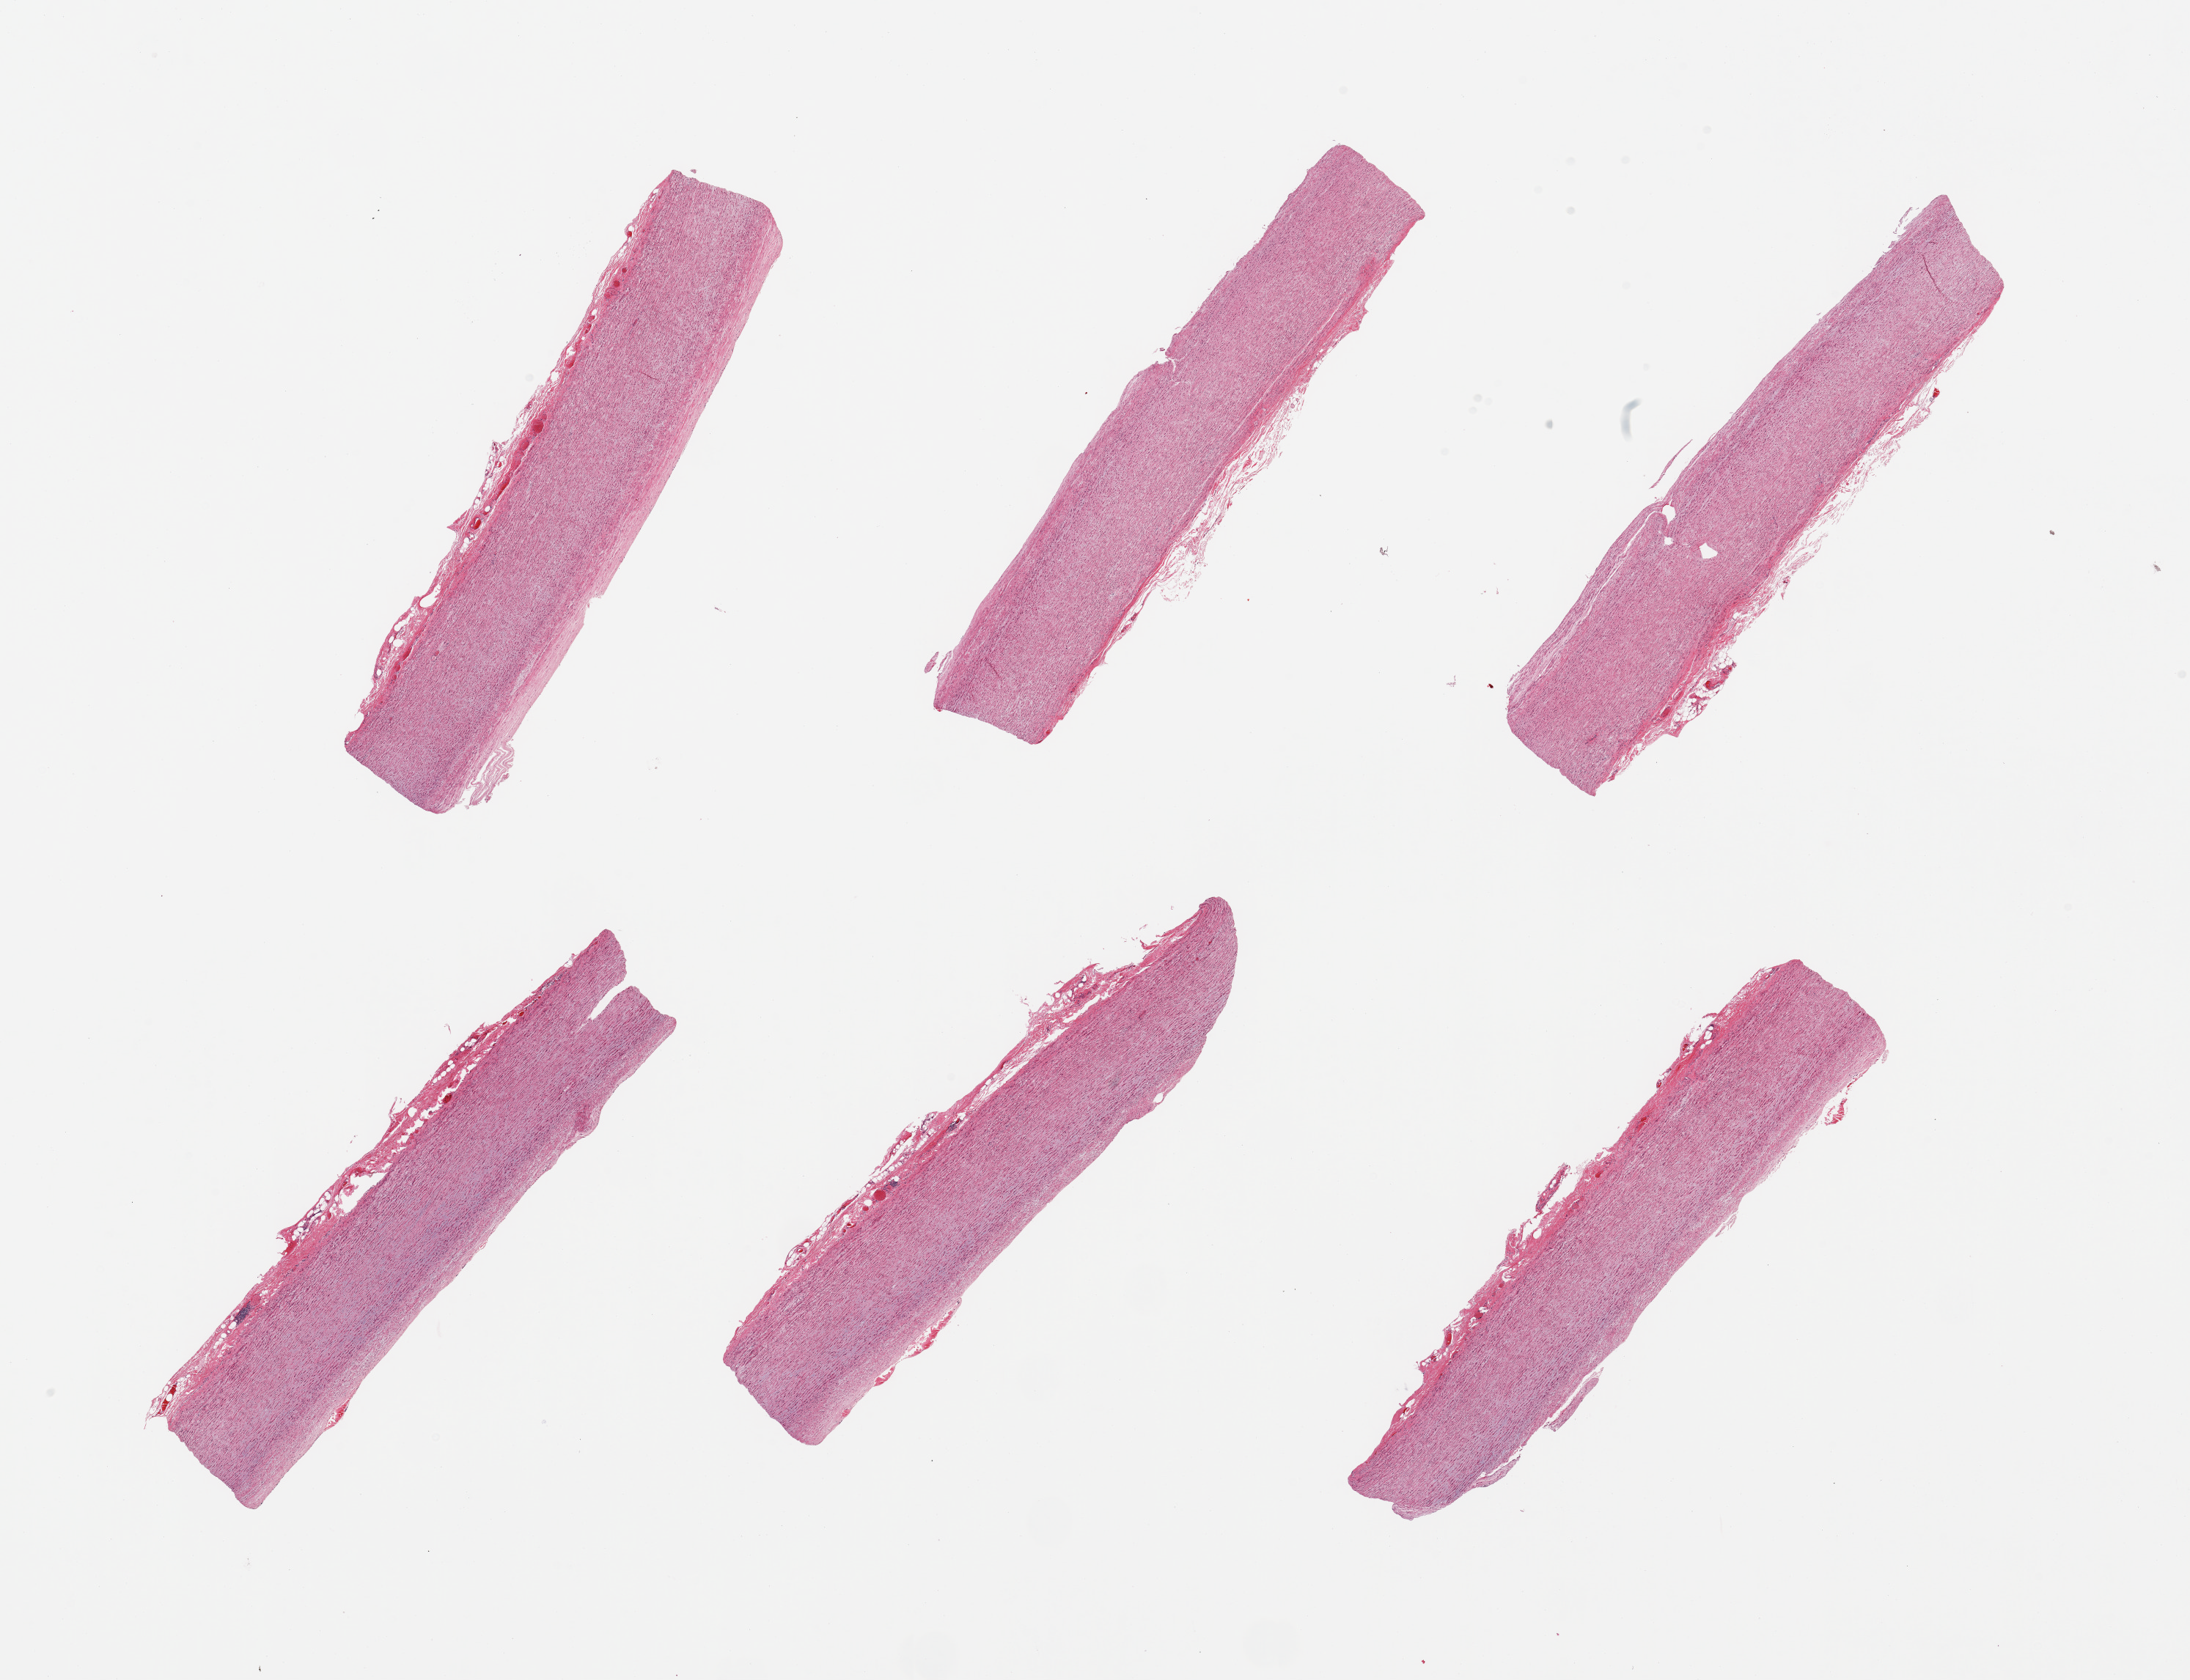
Hematoxylin and eosin (H&E) whole-slide image, a low-resolution overview of the entire scanned area, about 23.6 x 18.1 mm. PAXgene-fixed, paraffin-embedded tissue. Target tissue: aorta. Donor tissue sample. Female donor.
Review note (as recorded): 6 pieces; well trimmed; no plaques.